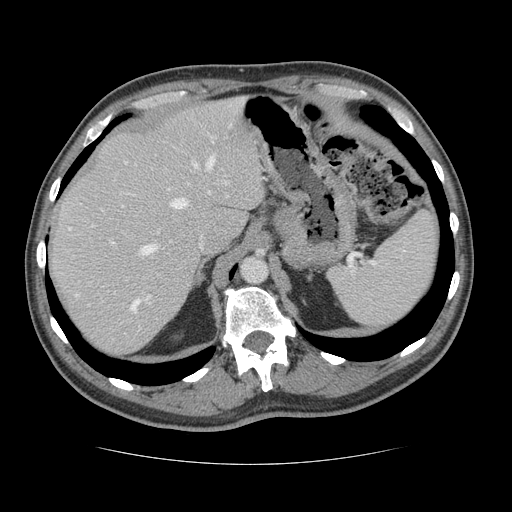
Contrast-enhanced abdominal CT, one axial slice; slice 96 of 134 in the series (ordered by position); reconstruction kernel STANDARD; intravenous contrast given; soft-tissue window (W 400 / L 40 HU); 512 × 512 image matrix, field of view 377 × 377 mm. Male patient, age 68 years. Case-level facts recorded for this patient, not image findings: diagnosis: colorectal cancer liver metastases, imaged before liver resection; multiple liver metastases: yes.
Annotated regions visible in this slice (expert manual segmentation):
- hepatic veins: bounding box <76,157,214,311> (left, top, right, bottom; pixels)
- liver: <51,100,264,356>
- planned liver remnant (the part of the liver to remain after resection): <50,99,265,330>
- portal vein (with intrahepatic branches): <111,182,227,297>